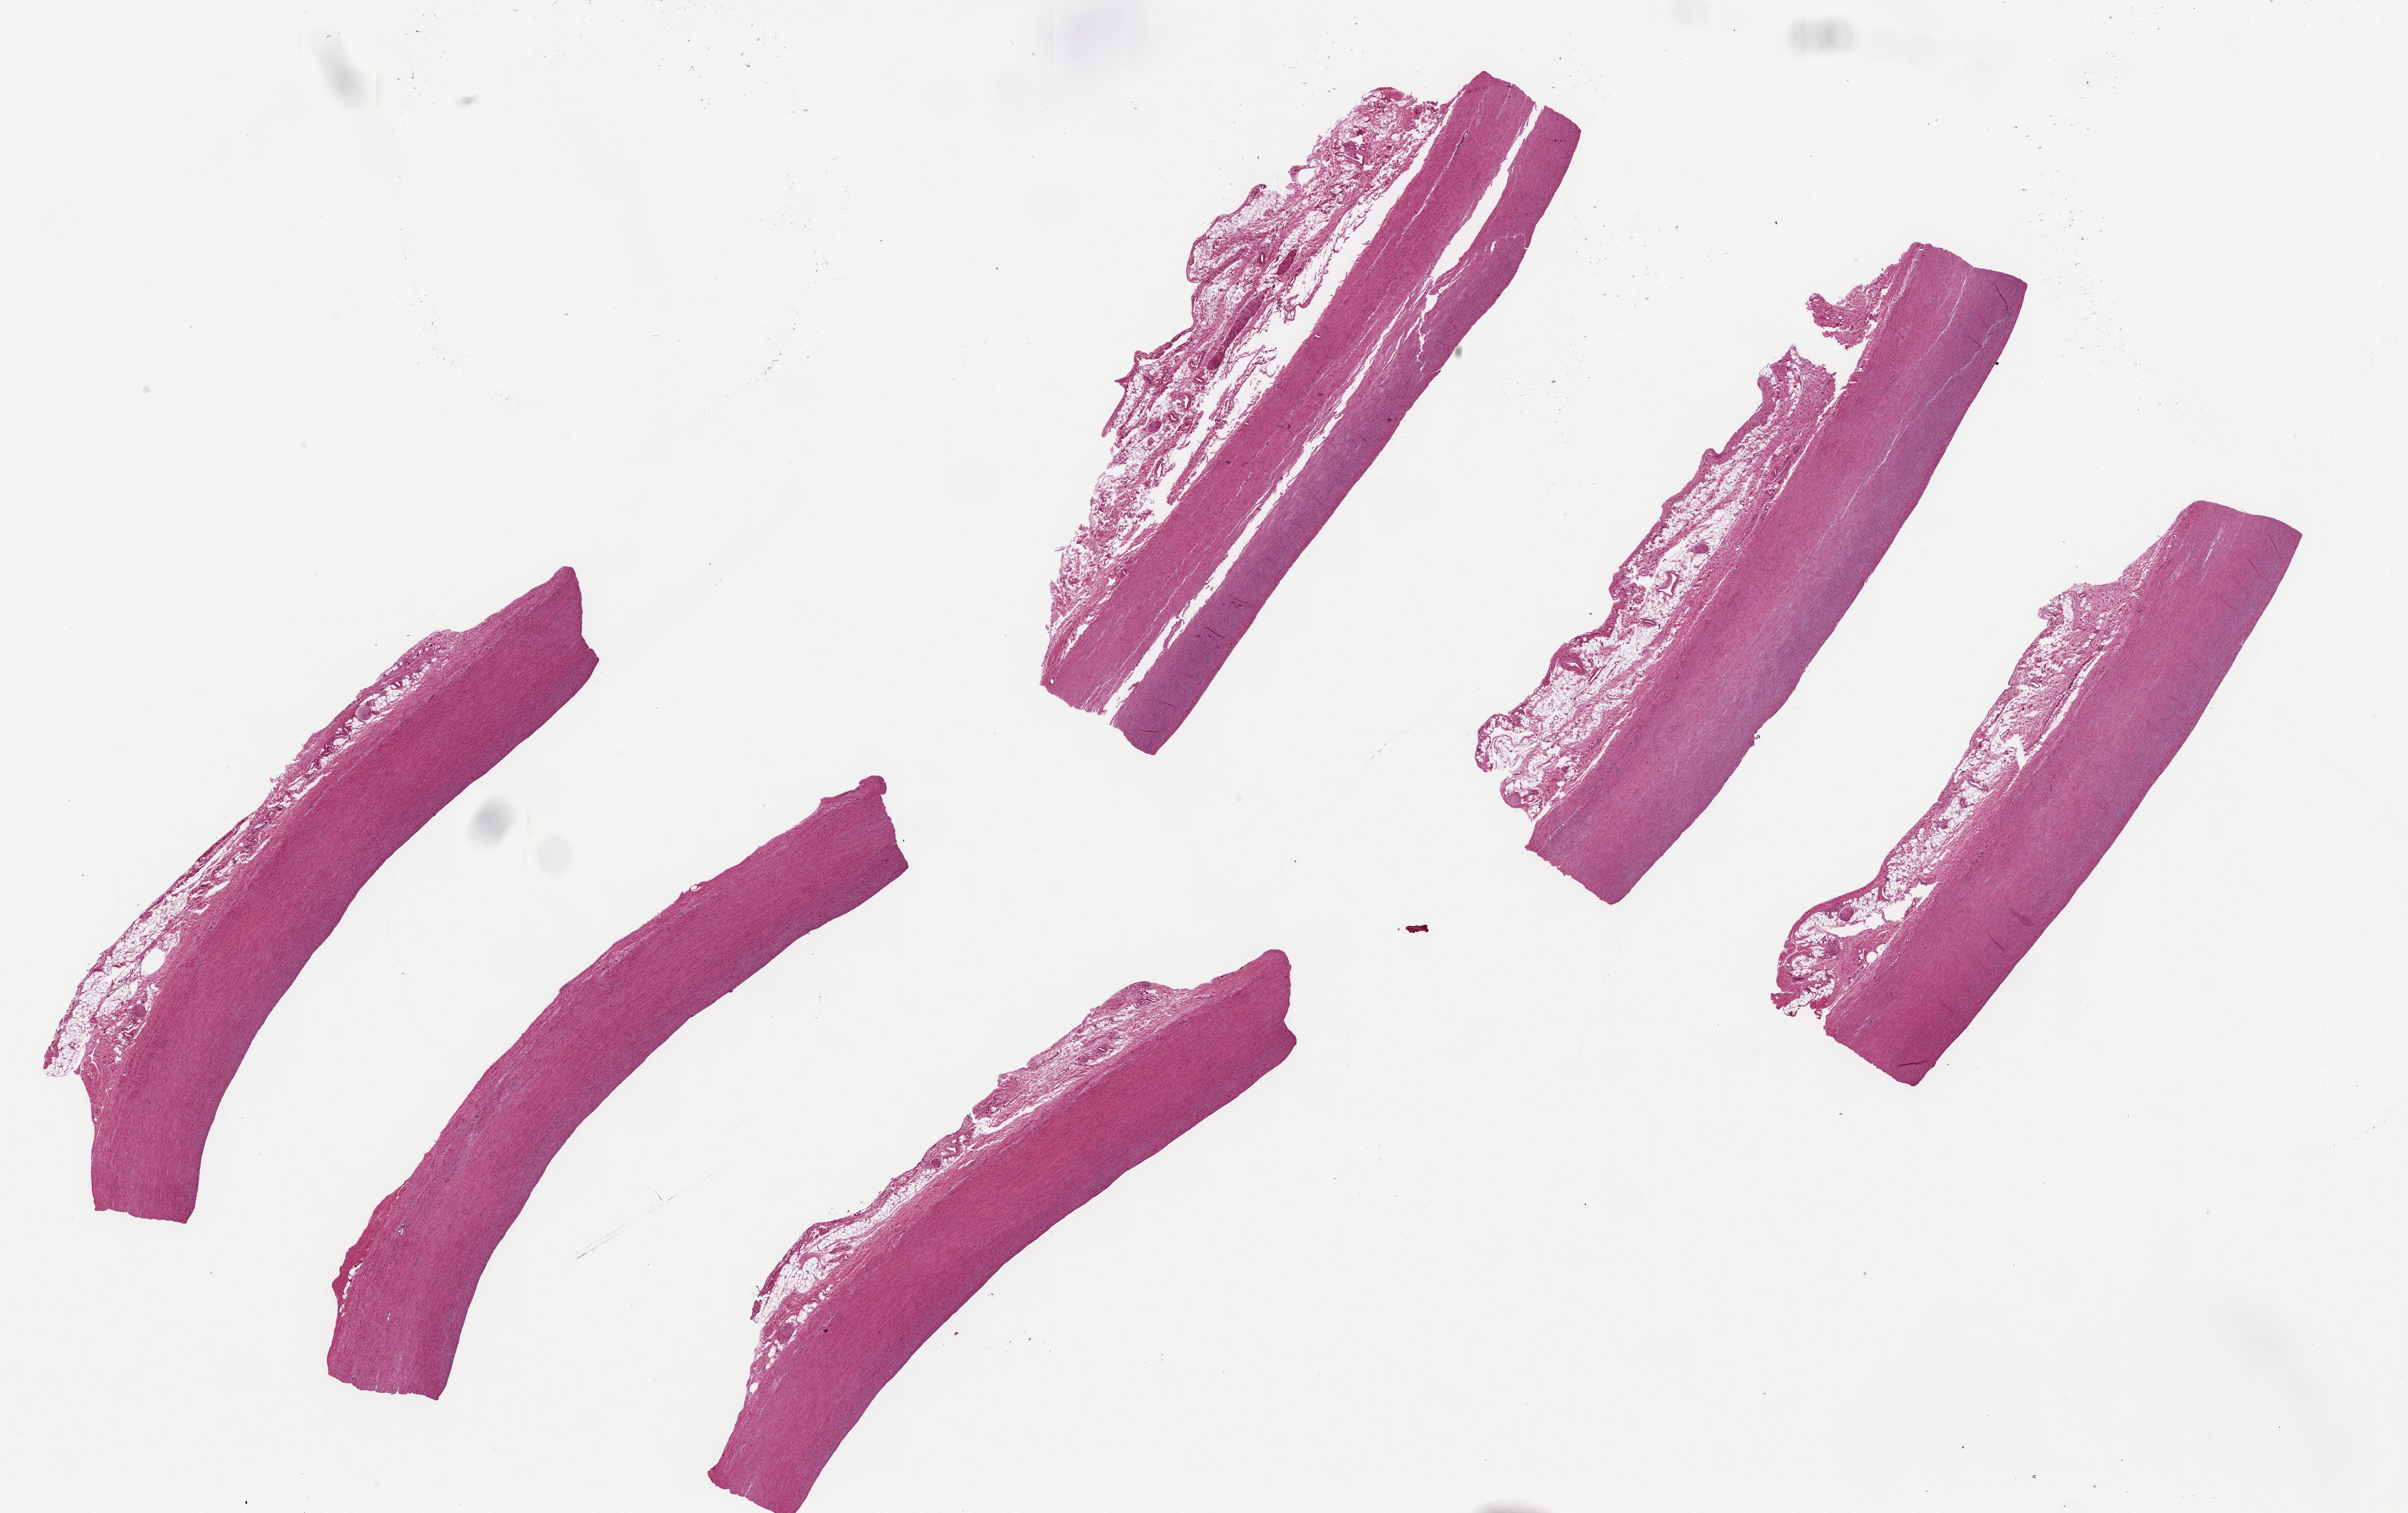
Digitized H&E-stained section — low-resolution overview of the scanned area, about 31.5 x 19.8 mm; PAXgene-fixed, paraffin-embedded tissue; section of aorta (target tissue); tissue donor sample. Donor sex: female.
* pathologist's review note for this sample: 6 pieces, 10x1.3mm